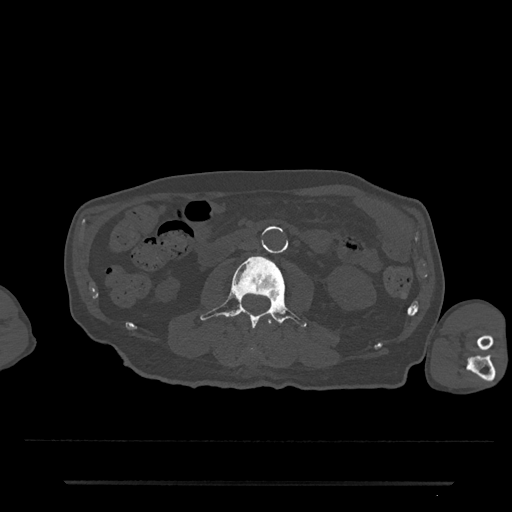
CT including the spine, one axial slice. Reconstruction kernel Br40s/3. 120 kVp. Bone window (W 1800 / L 400 HU). 0.5 mm slice thickness. 512 × 512 image matrix. Patient: male, 74 years. From the clinical record (not read from this slice): primary cancer: prostate.
Outlined on this slice (semi-automatic segmentation, software-assisted and operator-edited):
- L2 vertebra: bounding box [x1, y1, x2, y2] px = [246, 315, 275, 359]
- L3 vertebra: [200, 256, 307, 328]